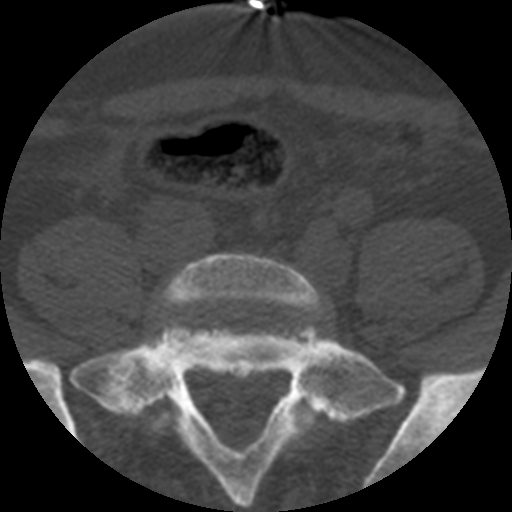
CT including the spine, one axial slice; slice 49 of 508 in the series (ordered by position); reconstruction kernel STANDARD; 120 kVp; bone window (W 1800 / L 400 HU); 1.25 mm slice thickness; 512 × 512 image matrix, field of view 160 × 160 mm. Patient age 57 years. Case-level facts recorded for this patient, not image findings: primary cancer: prostate.
Annotated regions visible in this slice (semi-automatic segmentation, software-assisted and operator-edited):
- L5 vertebra: bounding box <151,254,324,433> (left, top, right, bottom; pixels)